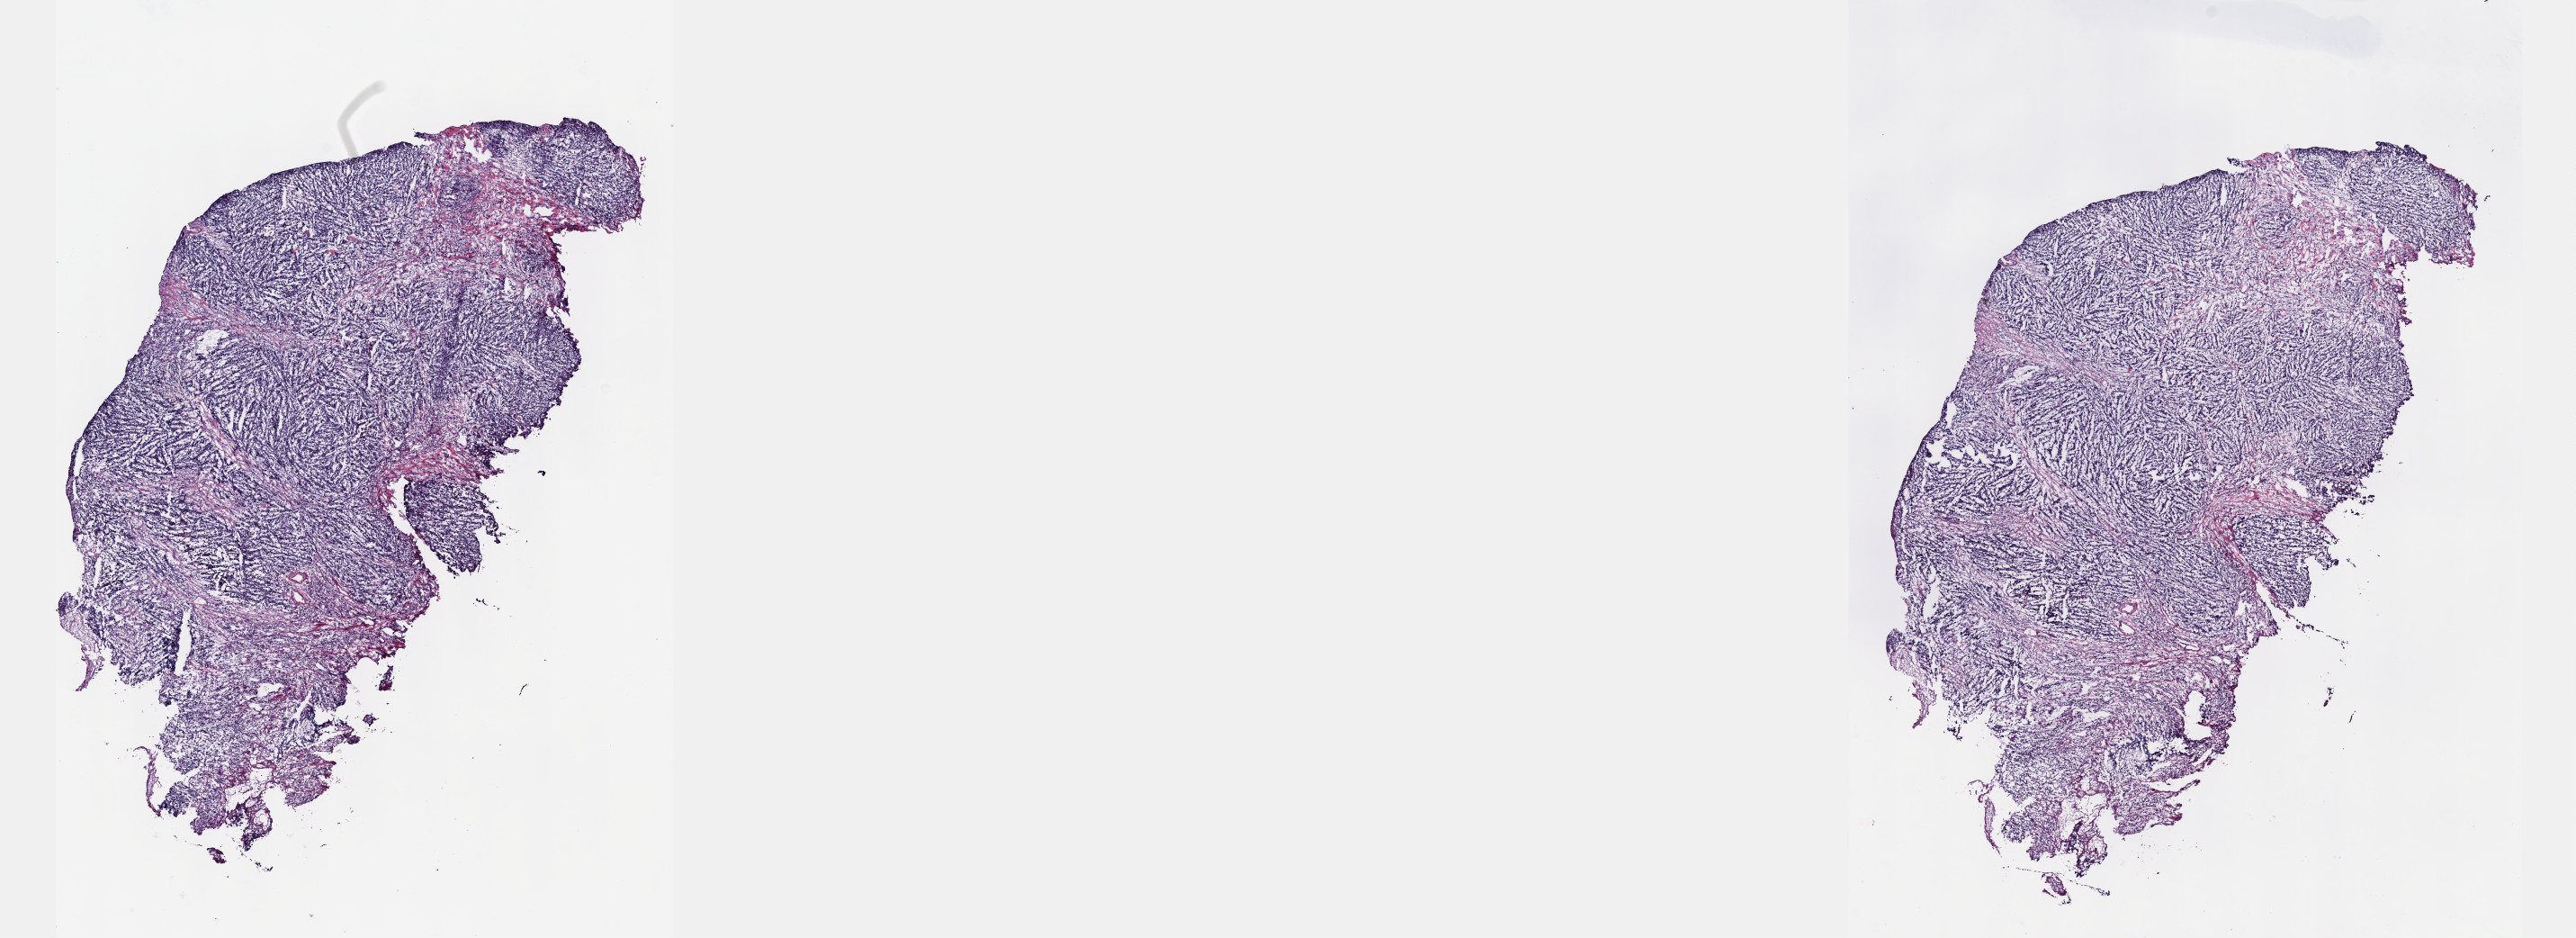
H&E whole-slide image, low-resolution overview of the scanned area, about 23.1 x 8.4 mm (slide scanned at 40x); frozen section from the top of the tissue portion; sample: primary tumour, esophagus. Male patient; age at initial diagnosis 49 years. Slide review estimates, as recorded: tumour cells 50%, tumour nuclei 70%.
Histologic diagnosis: Squamous cell carcinoma, NOS (lower third of esophagus).